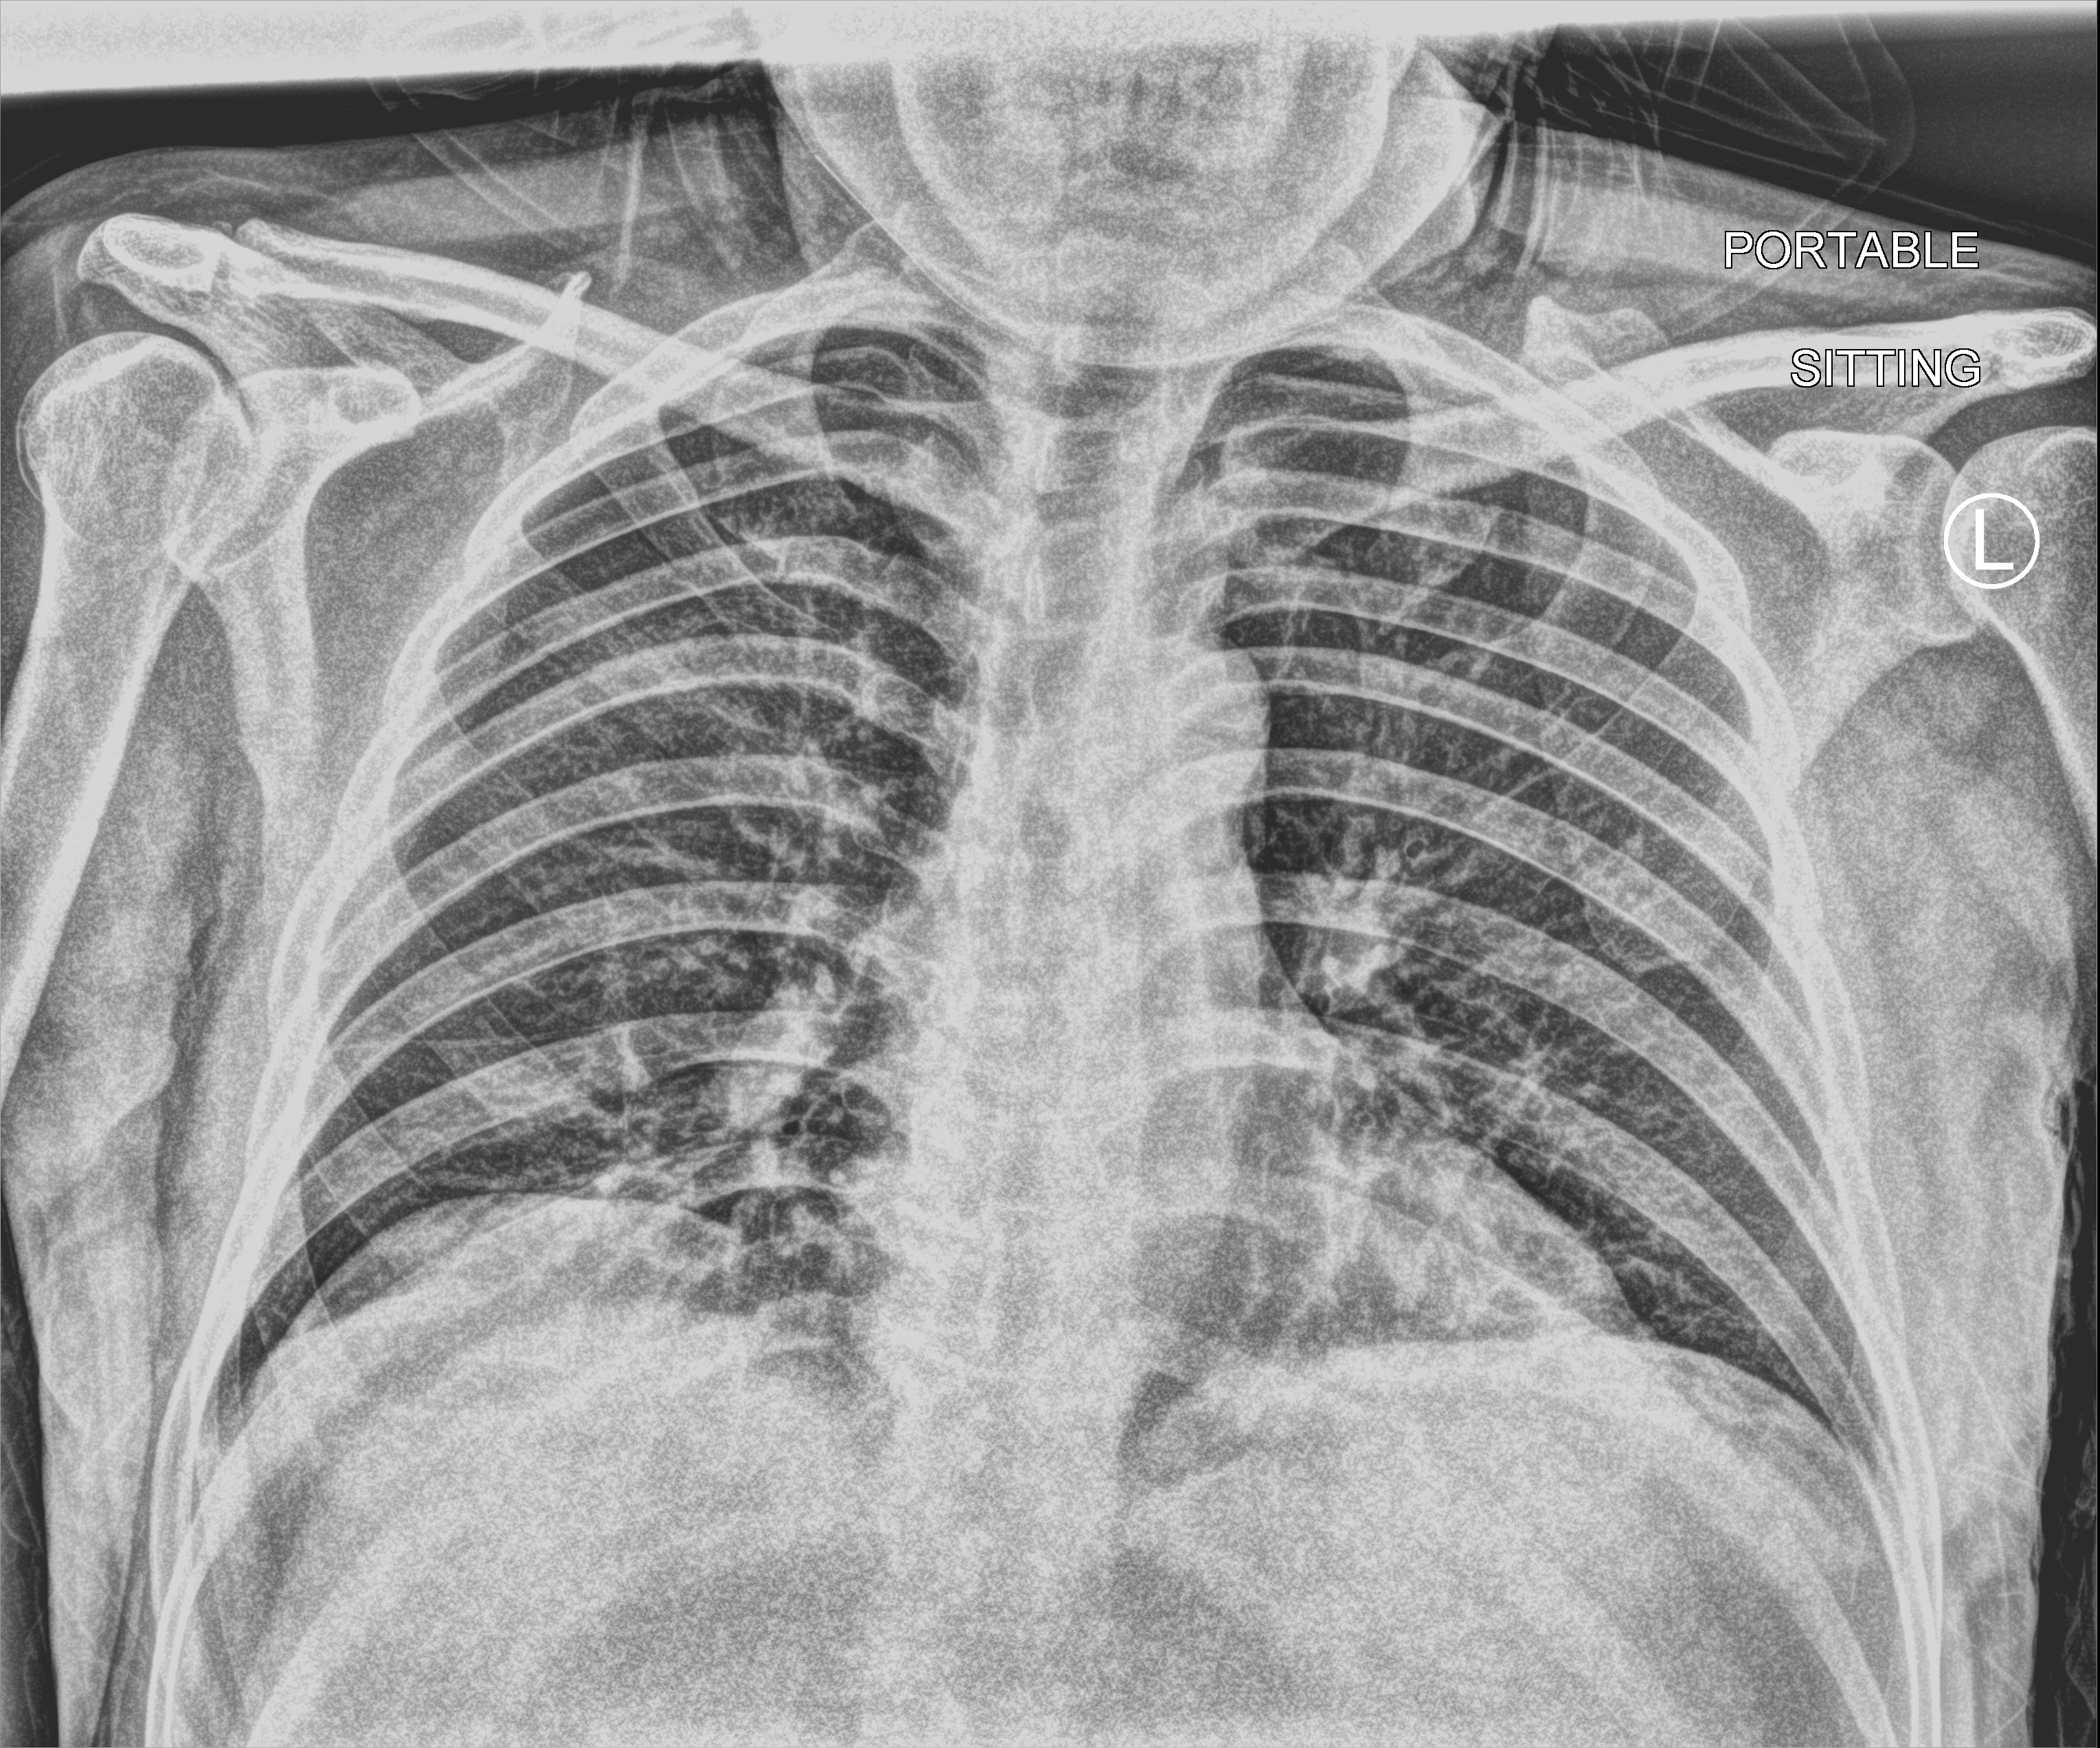
Bedside chest radiograph (computed radiography), anteroposterior (AP) projection. Male patient hospitalised with COVID-19, age 18–59 years.
Admission-level facts for this patient (not findings on this image; timing relative to this image not recorded): mechanically ventilated during this hospital stay: no; diabetes (admission record): no; length of hospital stay: 1 day.